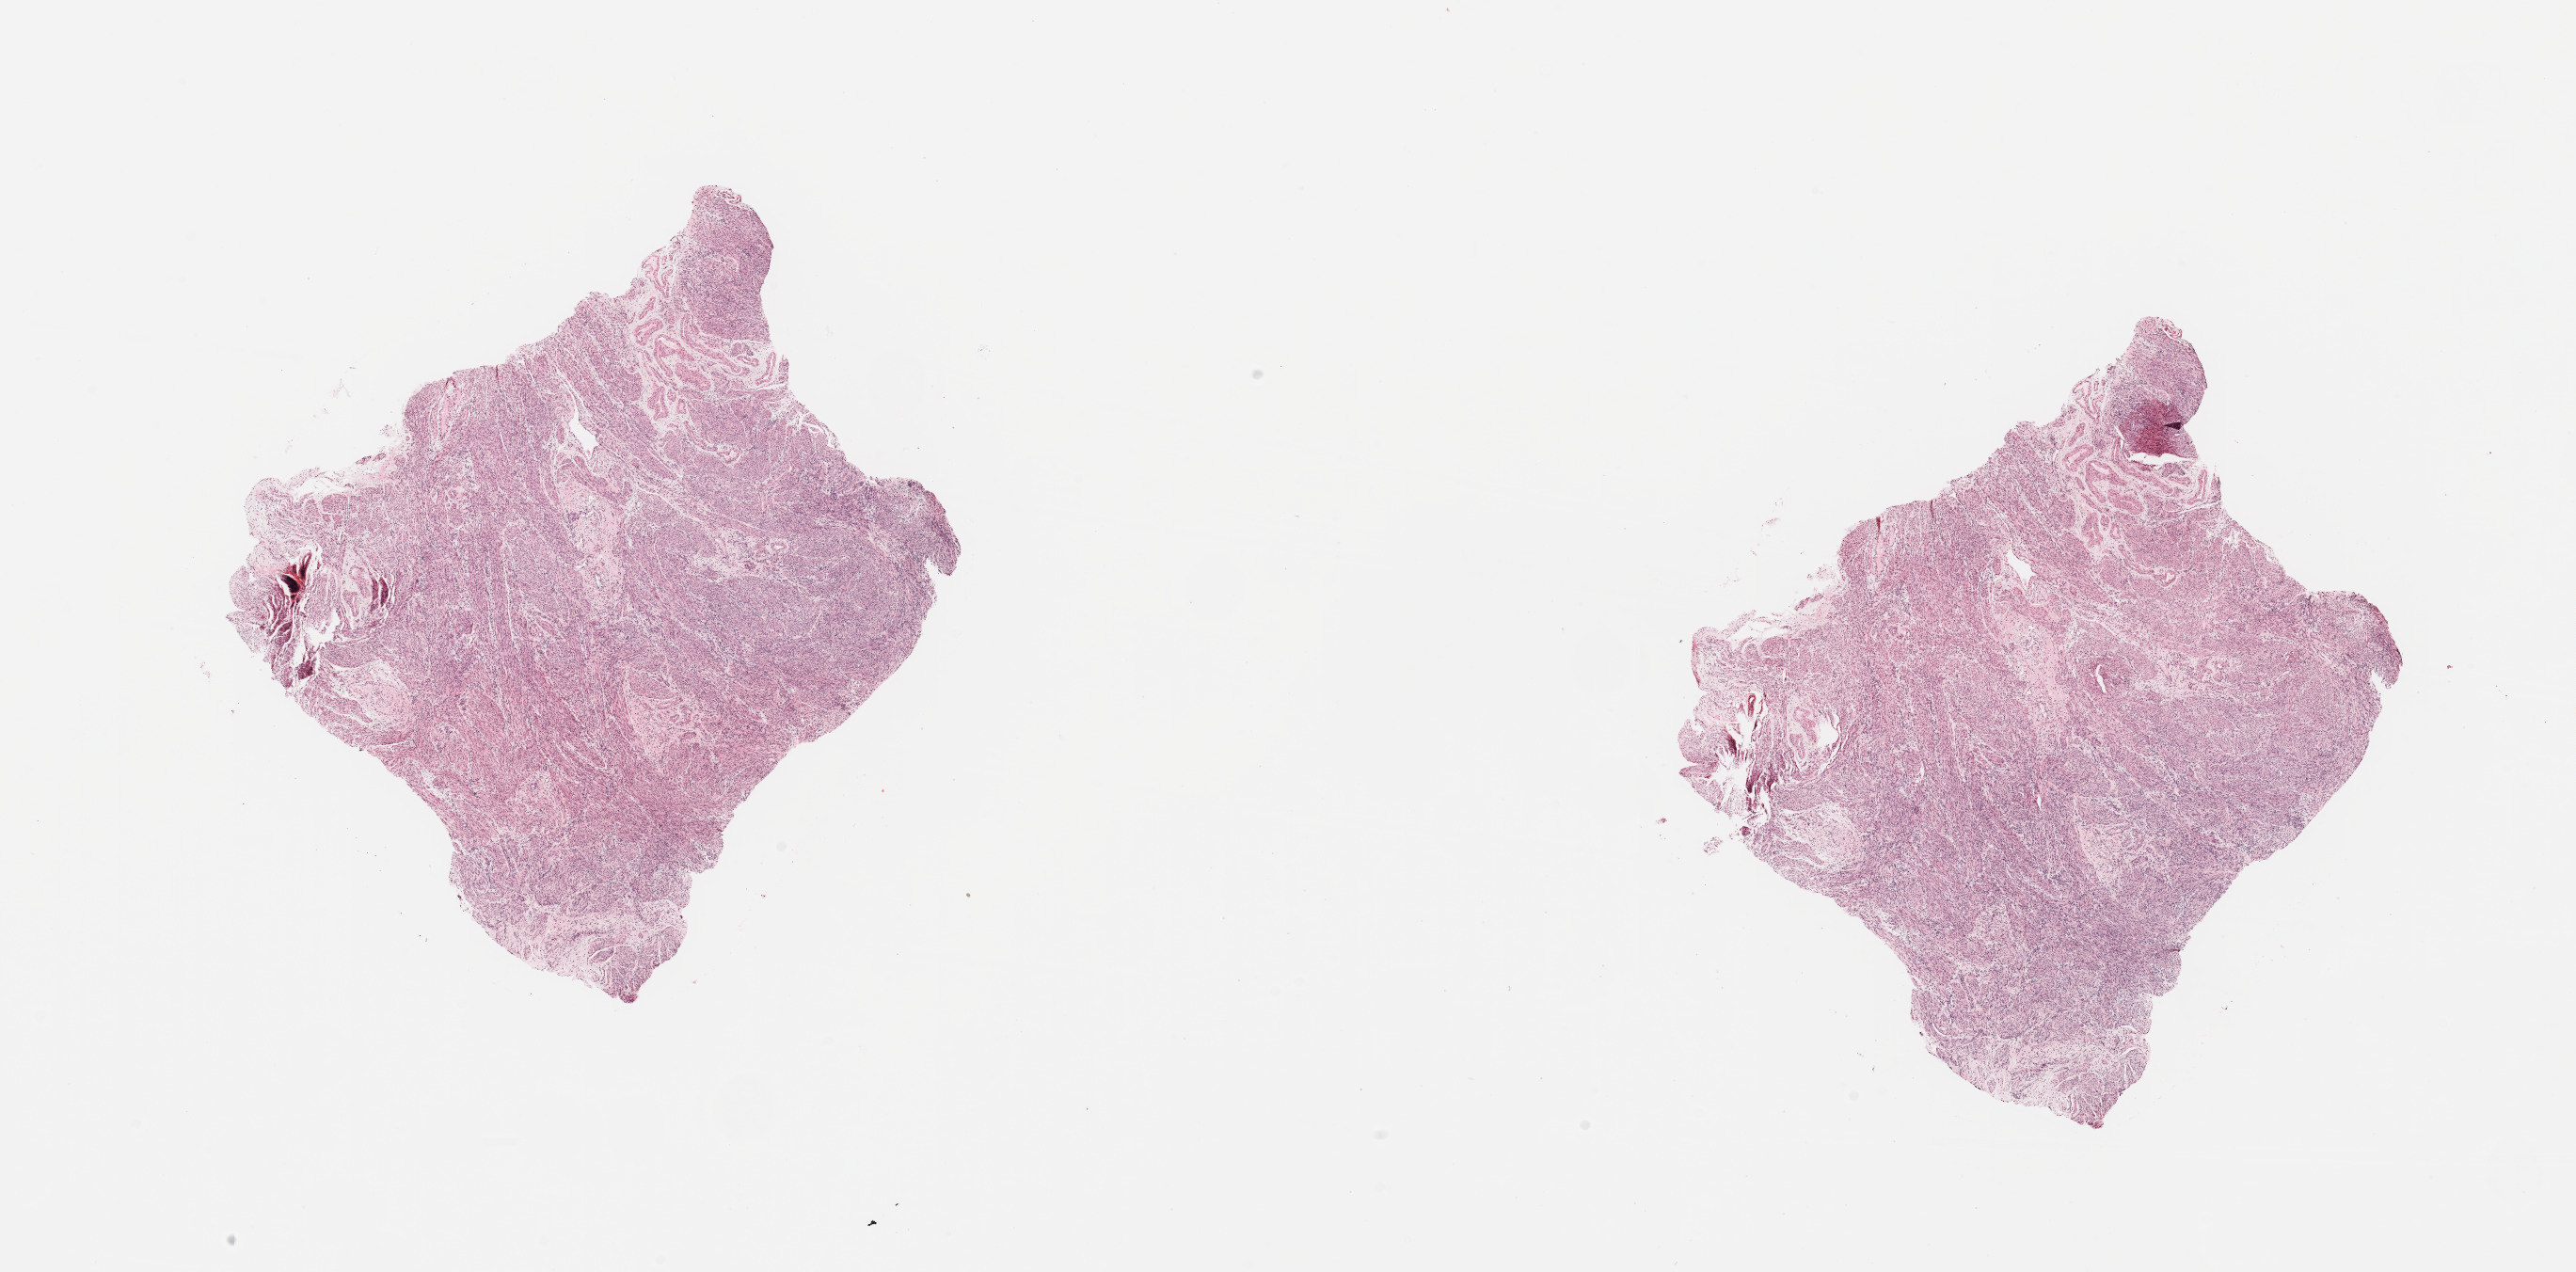
Digitized H&E-stained tissue section (whole slide), whole scanned area (about 21.7 x 10.7 mm, slide scanned at 20x) shown as a low-resolution overview, normal (non-tumour) tissue sample, uterus. Patient: female, age 81 years.
This section: normal (non-tumour) tissue from the same patient. Patient diagnosis (cohort enrolment): corpus endometrial carcinoma (uterus).